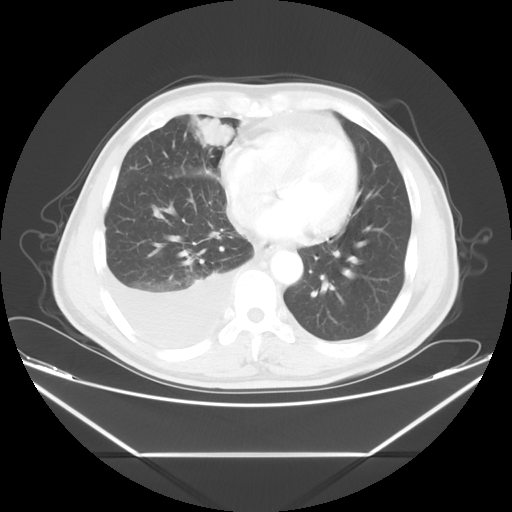
Chest CT, one axial slice. Position 19 of 56 along the scan axis. Reconstruction kernel STANDARD. Lung window (W 1500 / L -600 HU). 5 mm slice thickness. 512 × 512 image matrix, field of view 412 × 412 mm. Patient: male, 57 years. Case-level facts recorded for this patient, not image findings: clinical TNM (as recorded): T2 N3 M1.
Outlined on this slice (bounding box drawn by a radiologist):
- lung tumour (recorded histology: adenocarcinoma): box from (x=195, y=112) to (x=237, y=147) px